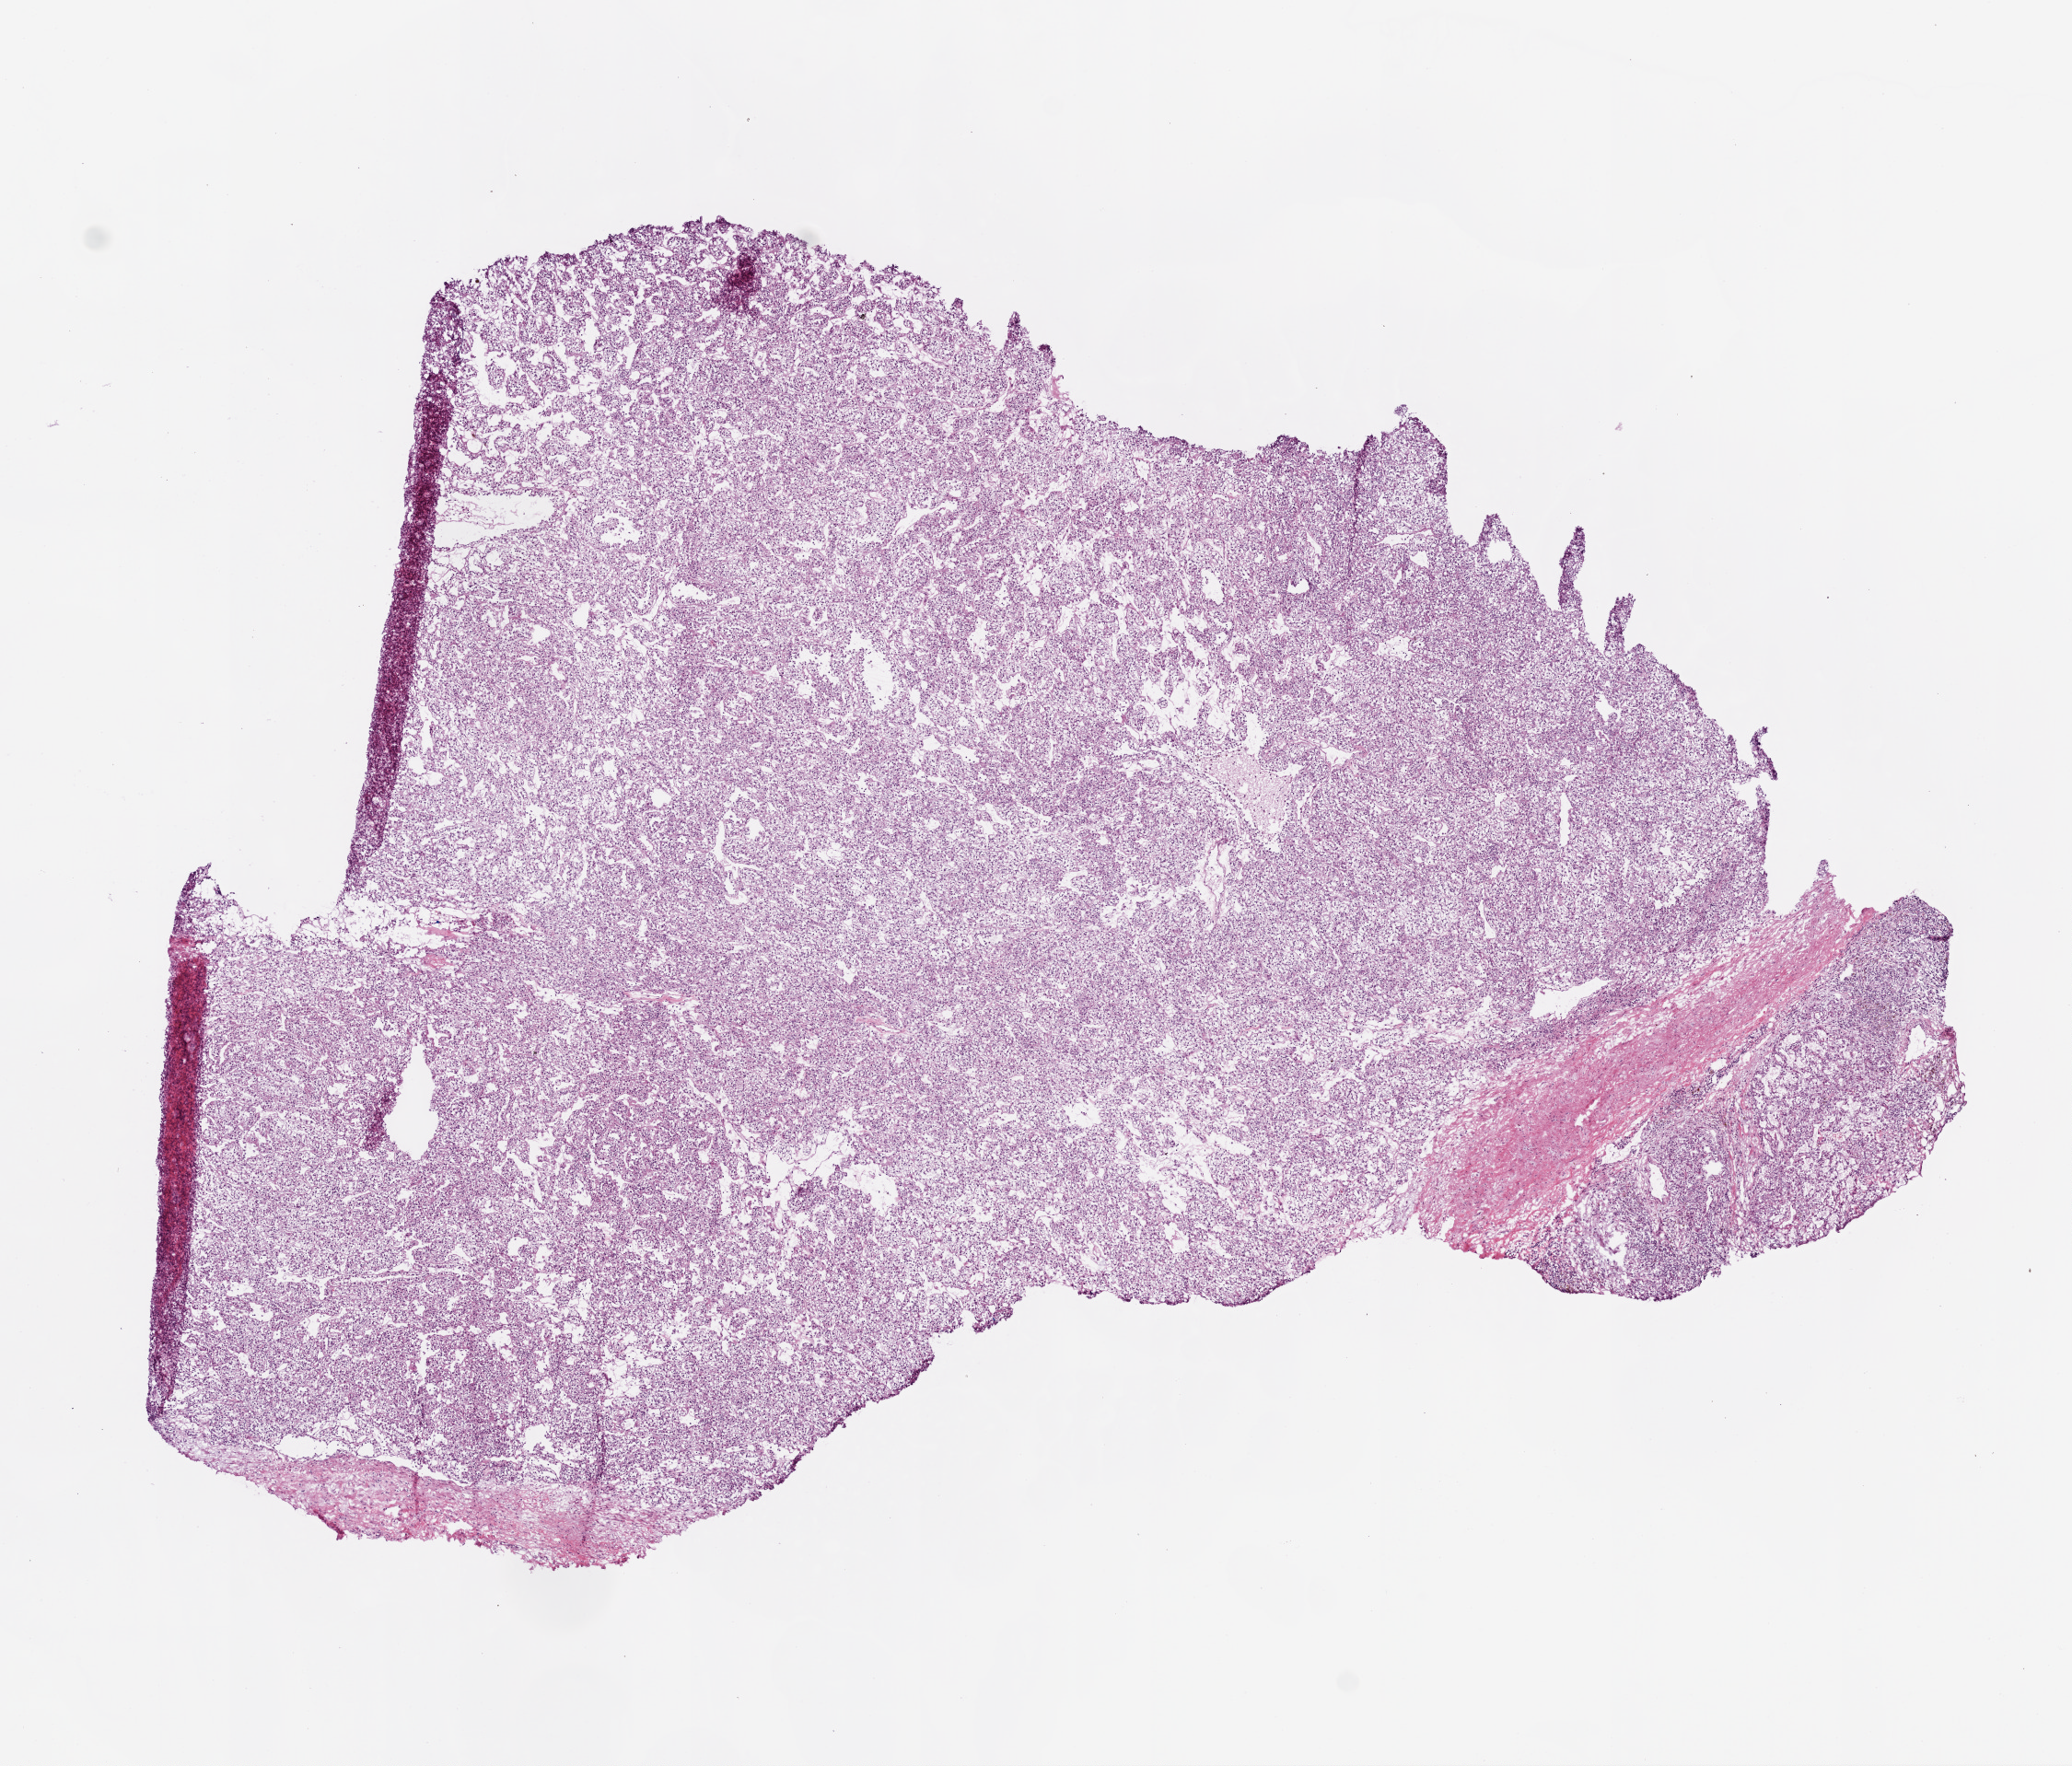
Digitized H&E tissue section (whole slide) — whole scanned area (about 9.0 x 7.7 mm) shown as a low-resolution overview. Frozen section from the top of the tissue portion. Kidney, primary tumour sample. Female patient; age at initial diagnosis 61 years. Histologic grade: G3 (poorly differentiated). Slide review estimates, as recorded: tumour cells 90%, tumour nuclei 90%, normal cells 0%, stromal cells 10%, necrosis 0%.
AJCC pathologic stage: I (7th edition). Histologic diagnosis: Clear cell adenocarcinoma, NOS.